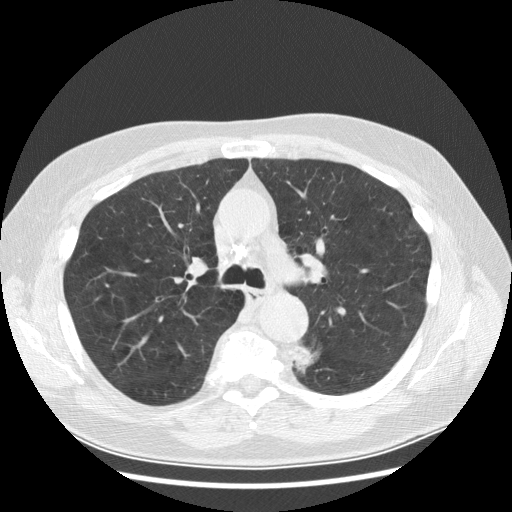
Axial slice from a low-dose chest CT screening exam. First (baseline) screen. Lung window (W 1500 / L -600 HU). 2.5 mm slice thickness. 120 kVp. Slice 93 of 282 in the series. Male, age 70 years at enrolment. Current smoker at enrolment.
Lesion marked by an expert reader, box from (x=277, y=338) to (x=325, y=379) px. Screening reader's record for this exam (one nodule recorded; not confirmed to be the boxed lesion): non-calcified nodule or mass ≥4 mm, left lower lobe, 27 × 16 mm, spiculated (stellate) margins, soft tissue attenuation, pre-existing on the prior screen: yes; interval growth: yes. Lung cancer was diagnosed 97 days after this screen: papillary adenocarcinoma, NOS, left lower lobe, moderately differentiated (G2), stage IB (AJCC 6th edition), 35 mm at pathology.